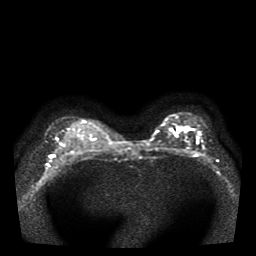
Breast MRI, one axial slice. Slice 27 of 41 in the series (ordered by position). Diffusion-weighted series; image 2 of 4 stored at this slice position (different b-values; order by instance number). 1.5 T. 5 mm slice thickness. 256 × 256 image matrix, field of view 330 × 330 mm. Female patient.
Outlined on this slice (manually delineated by an expert):
- tumour on diffusion-weighted imaging: bounding box (x1, y1, x2, y2) in pixels: (174, 127, 184, 135)